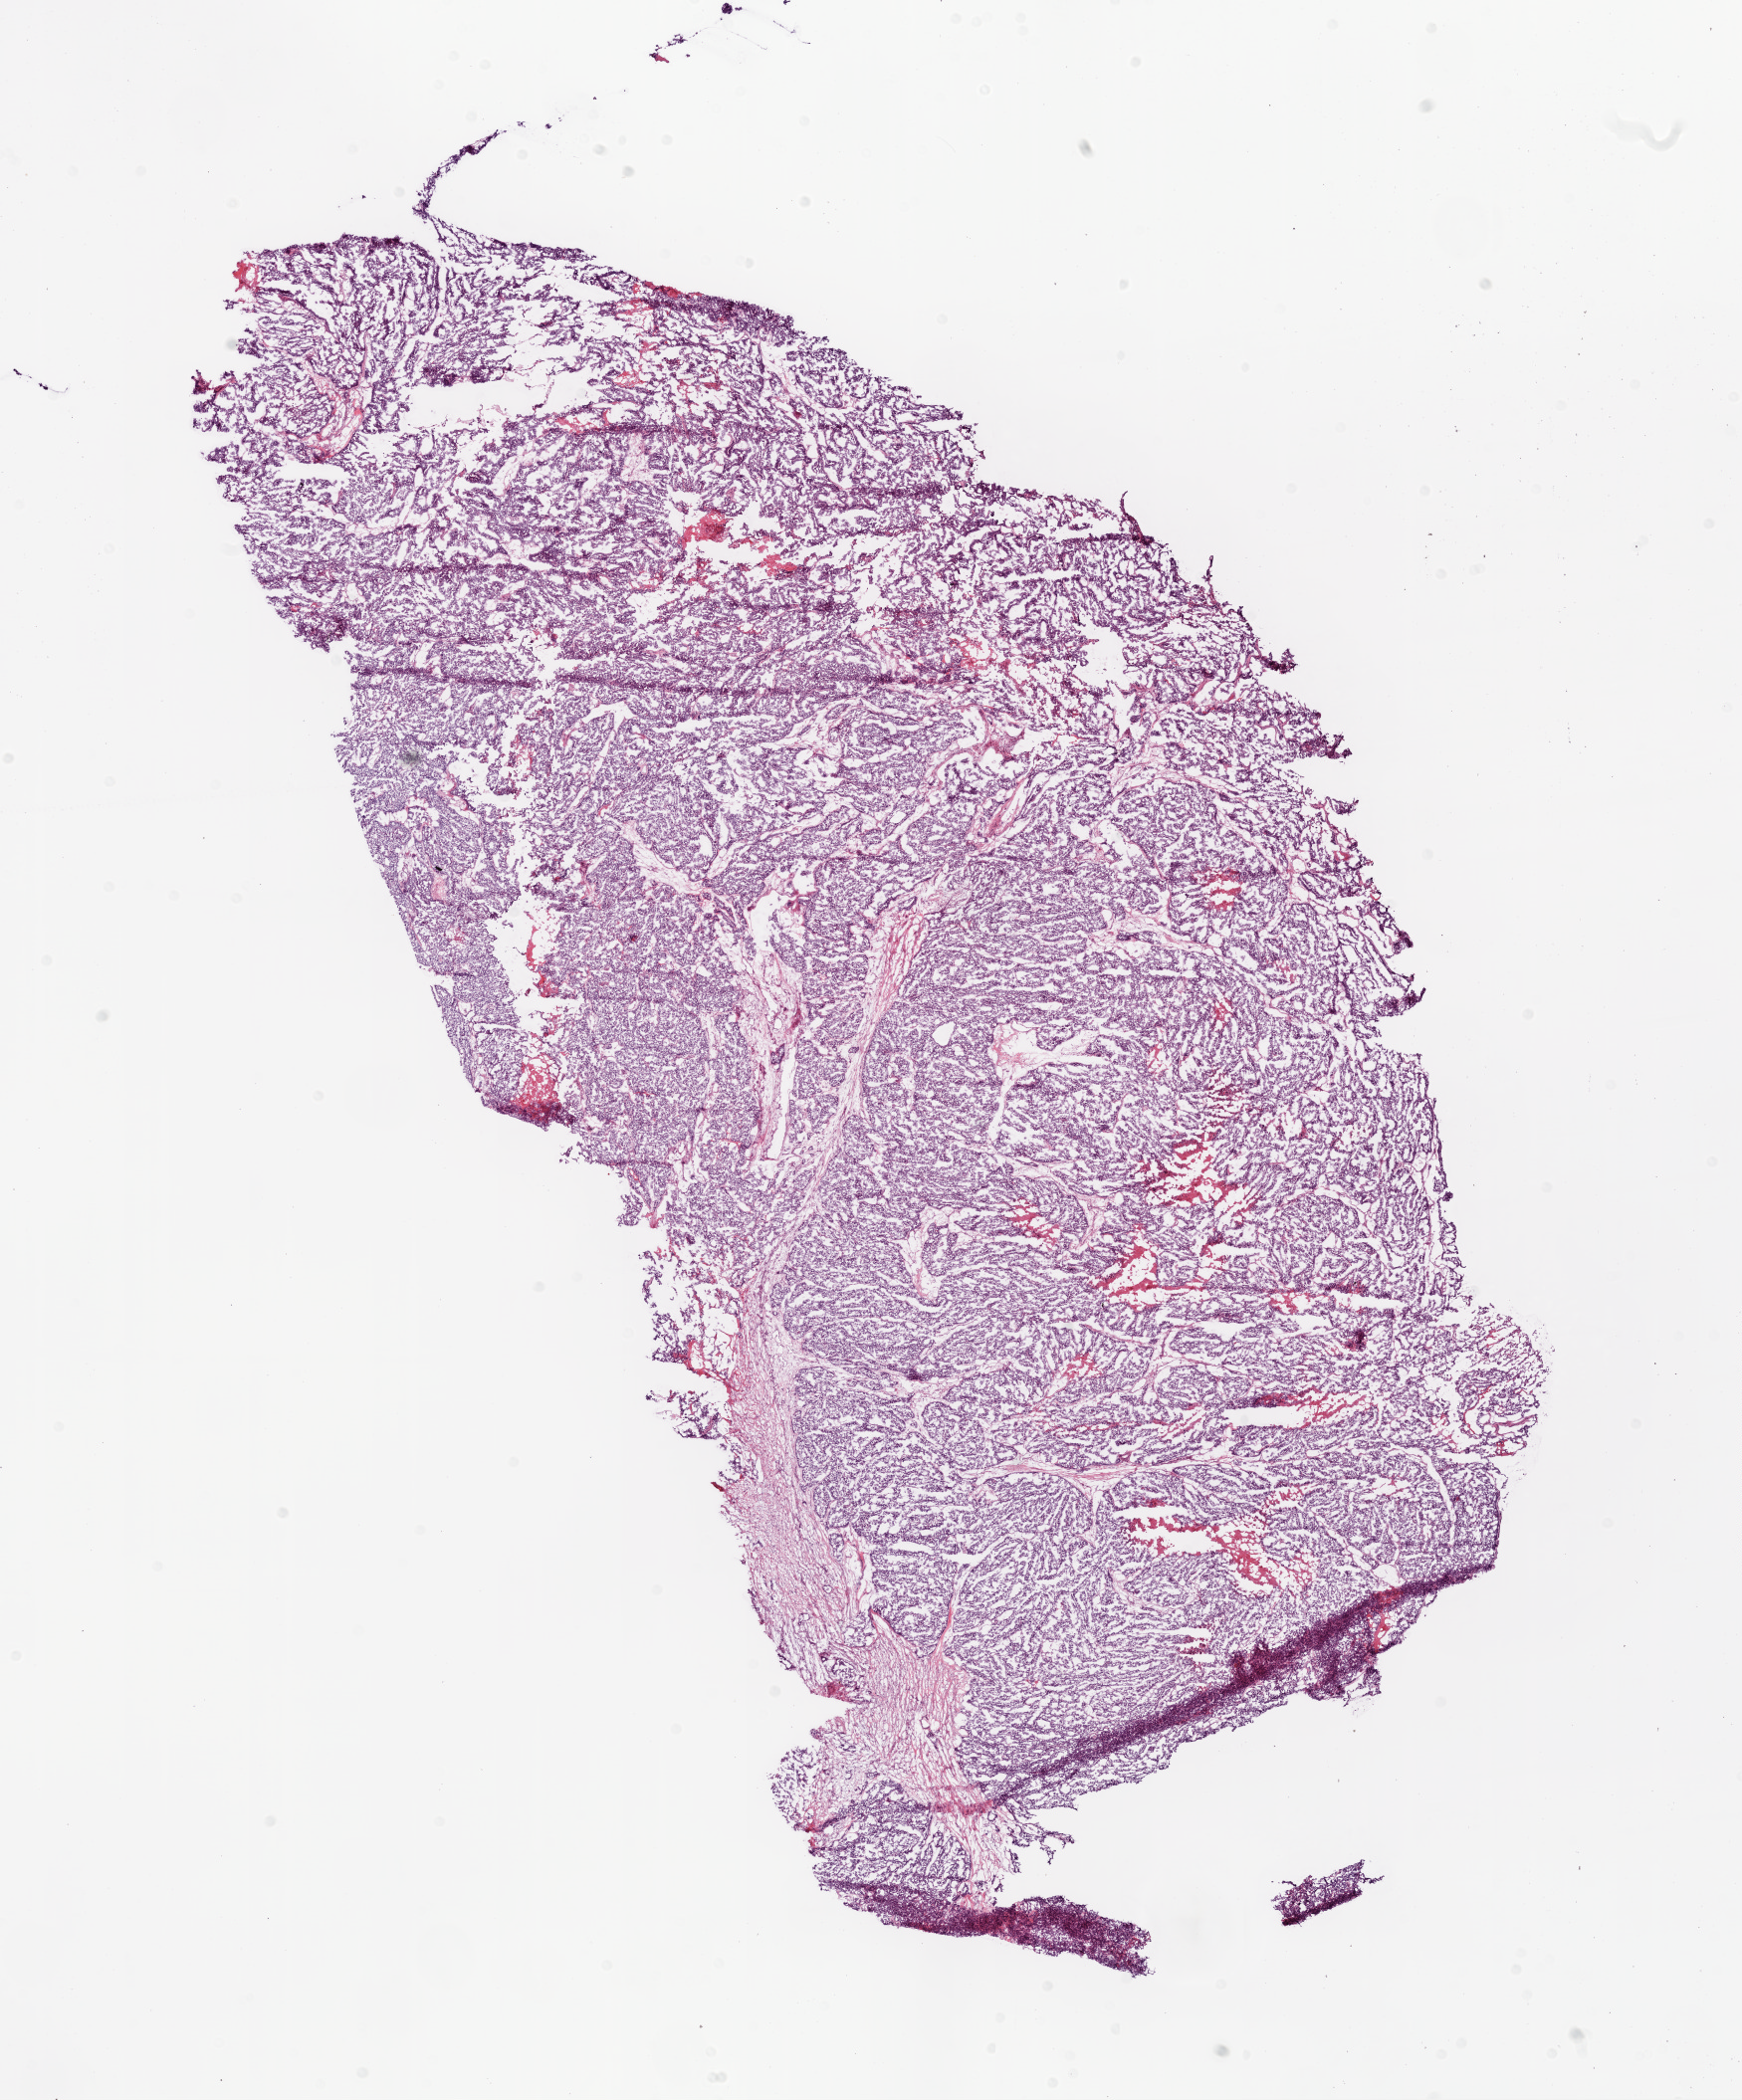
Whole-slide histology image, H&E-stained — low-resolution overview of the scanned area, about 14.0 x 16.9 mm (from a 20x scan); frozen section from the bottom of the tissue portion; ovary, primary tumour sample. Patient: female, age at initial diagnosis 67 years. Histologic grade: G3 (poorly differentiated). Pathologist review of this section (percent, as recorded): tumour cells 90%, tumour nuclei 95%, normal cells 0%, stromal cells 5%, necrosis 5%. Infiltration values recorded for this section: lymphocyte infiltration 0%, monocyte infiltration 0%, neutrophil infiltration 0%.
Pathologic diagnosis: Serous cystadenocarcinoma, NOS. Laterality: bilateral. FIGO stage: IIIC.